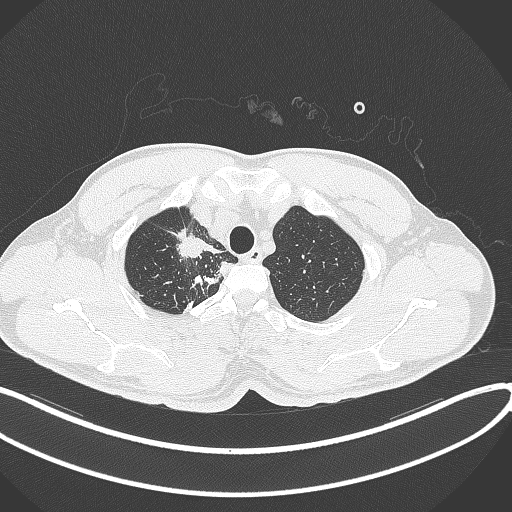
Chest CT, one axial slice; position 328 of 391 along the scan axis; reconstruction kernel B70f; 120 kVp; lung window (W 1500 / L -600 HU); 1 mm slice thickness; 512 × 512 image matrix, field of view 400 × 400 mm. Patient: male, 48 years. Case-level facts recorded for this patient, not image findings: clinical TNM (as recorded): T1c N1 M1.
Structures marked on this image (bounding box drawn by a radiologist):
- lung tumour (recorded histology: adenocarcinoma): bounding box <172,230,207,262> (left, top, right, bottom; pixels)